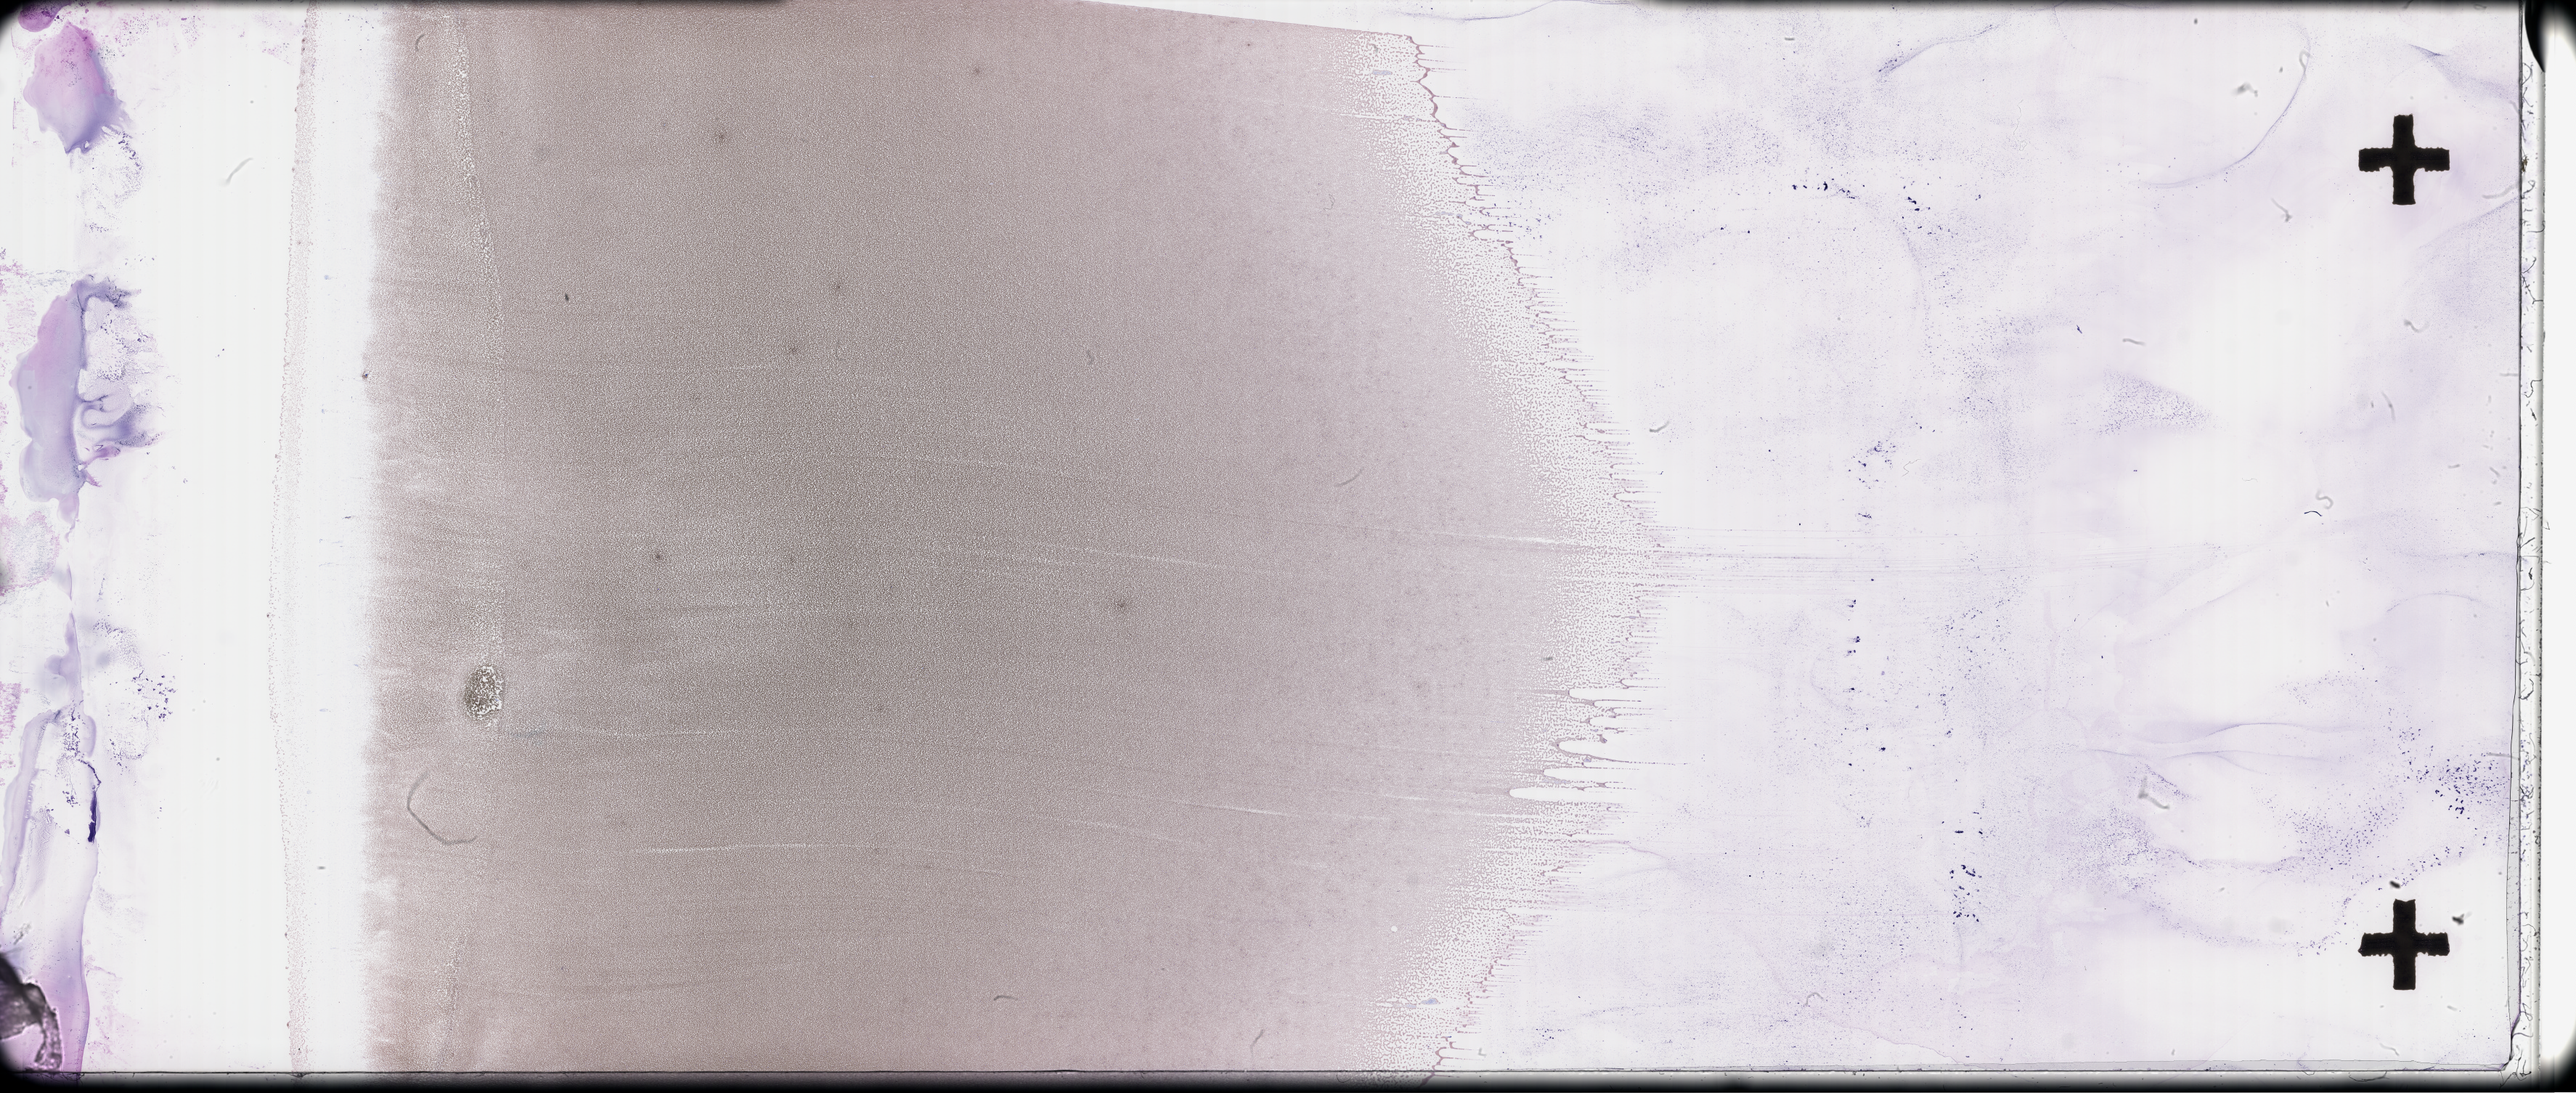
Whole-slide image of a whole blood smear, Wright-Giemsa stain — low-resolution overview of the scanned area, about 57.3 x 24.3 mm. EDTA-anticoagulated smear. Collected on treatment. Patient sex: female.
• from a patient with: Plasma Cell Myeloma